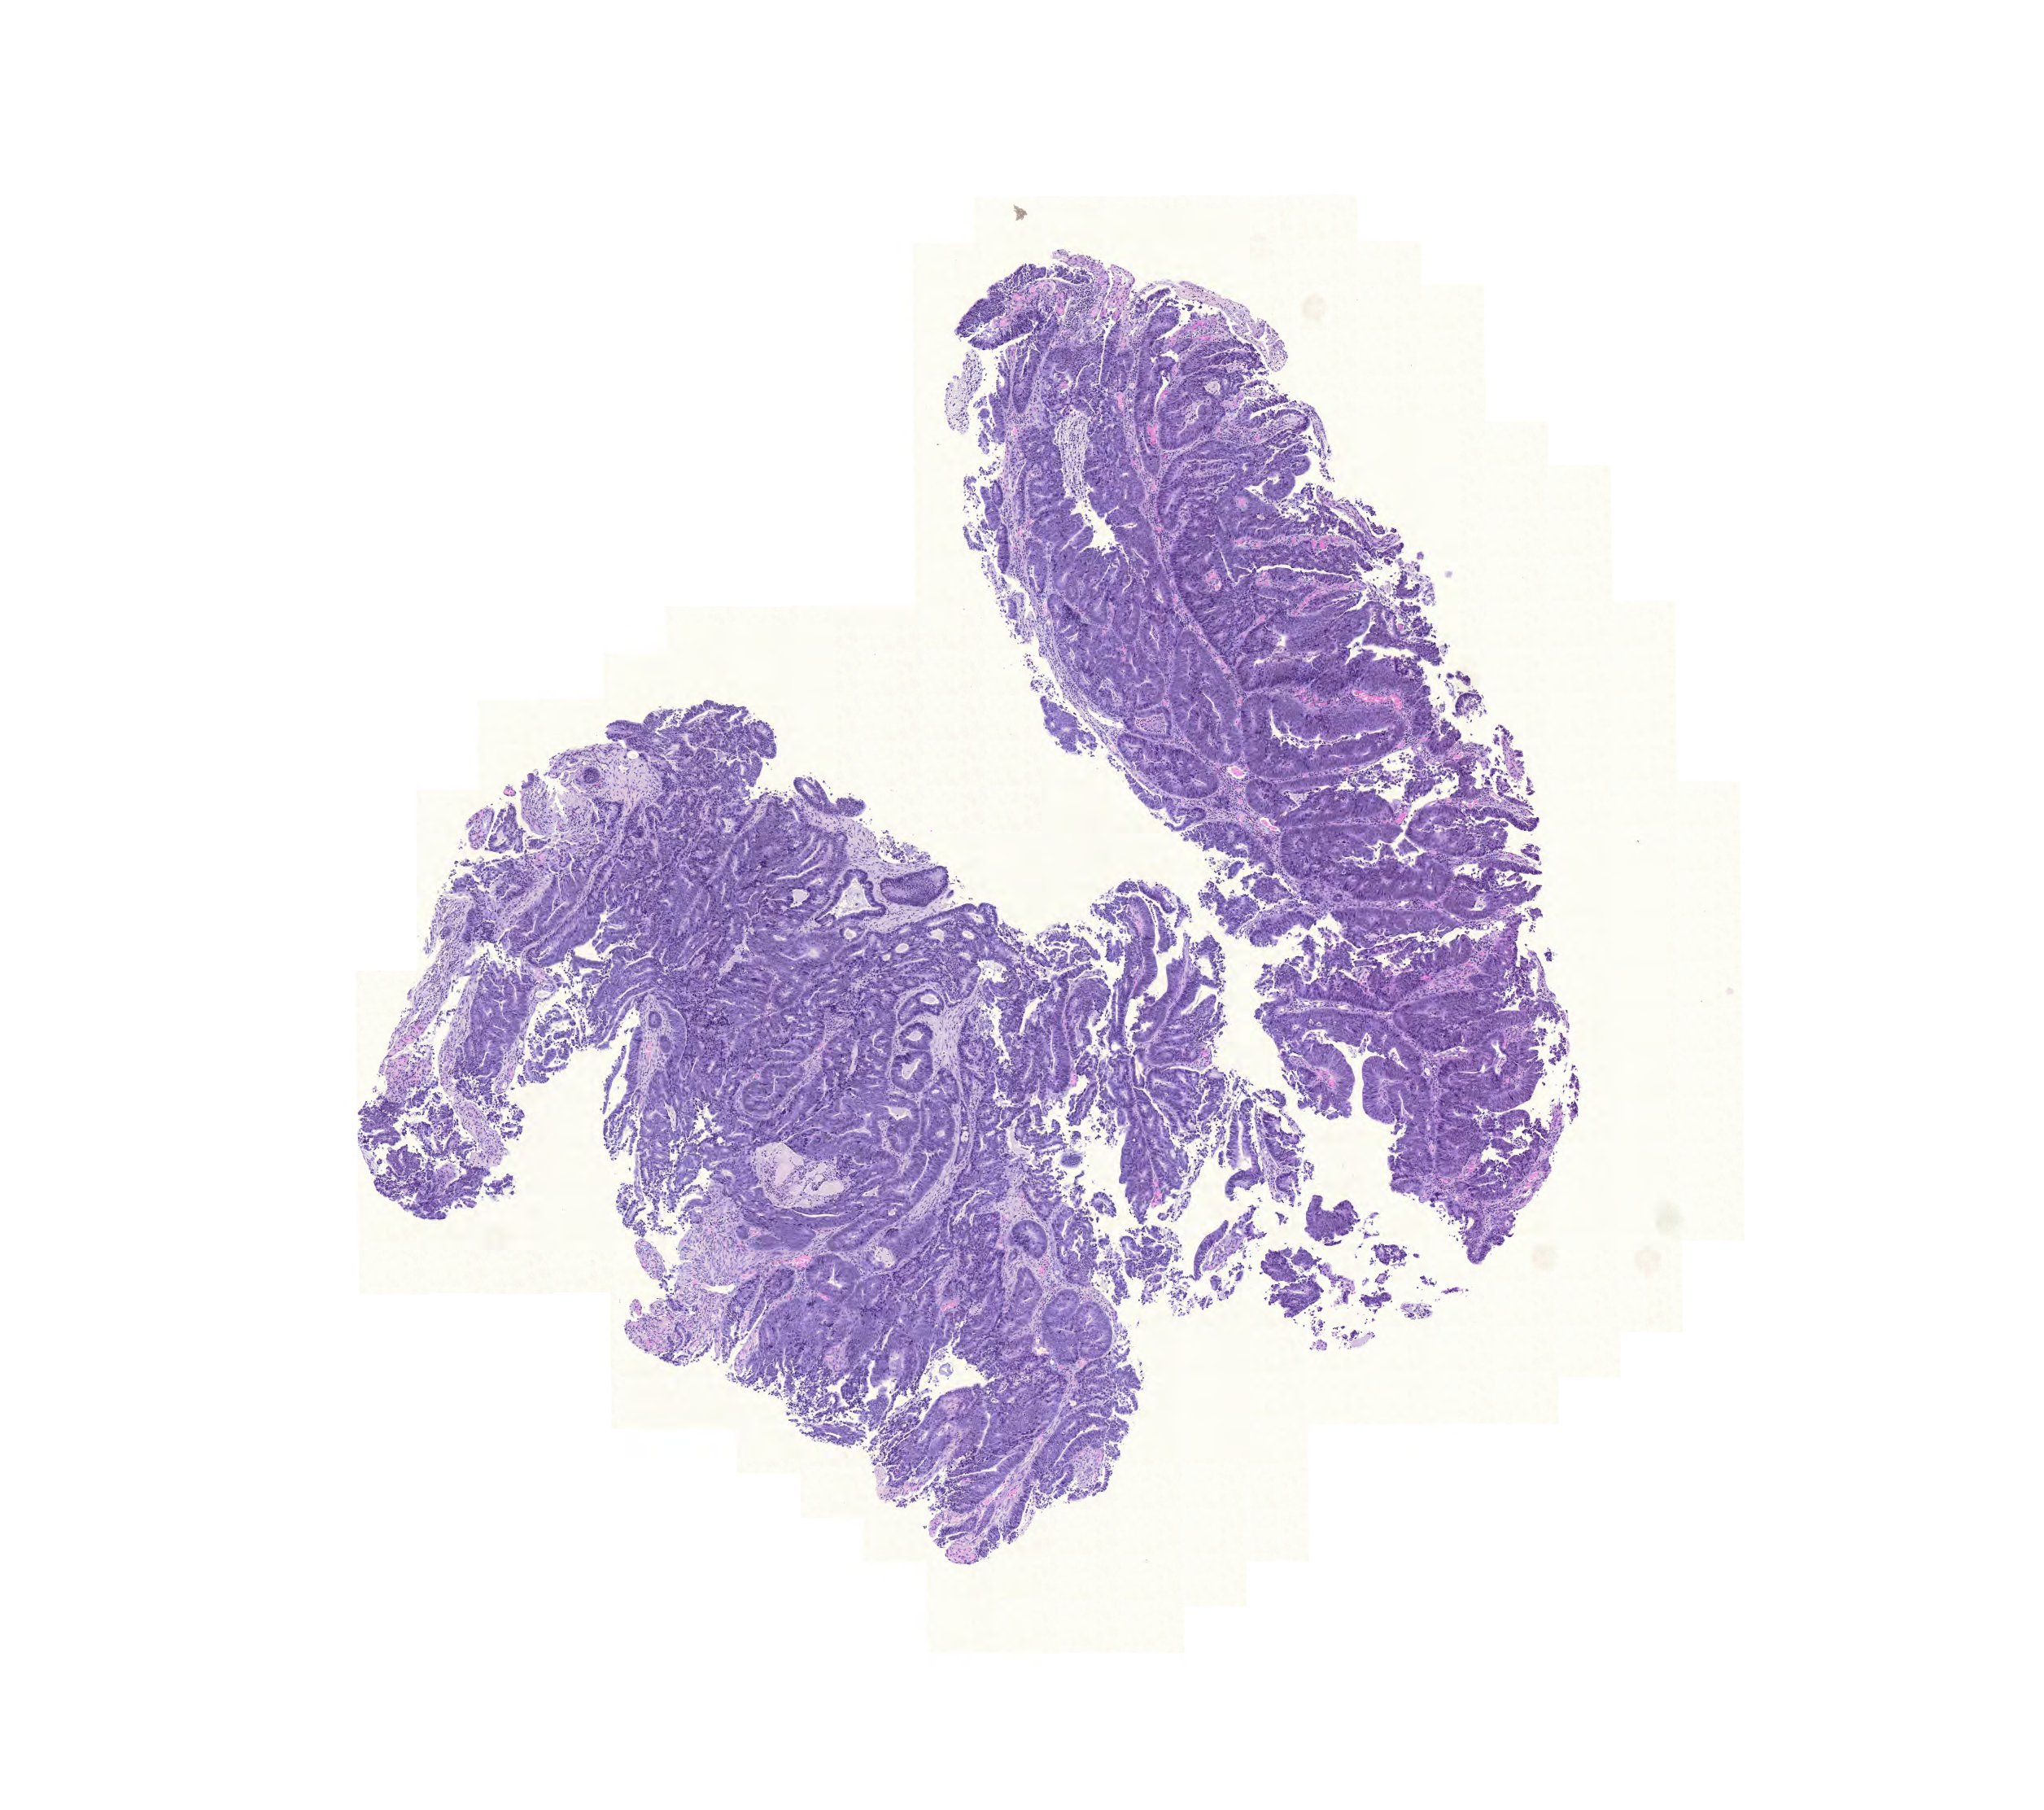
H&E whole-slide image — whole scanned area (about 9.3 x 8.3 mm, from a 20x scan) shown as a low-resolution overview. Formalin-fixed paraffin-embedded (FFPE) diagnostic section. Rectum, primary tumour sample. Male, age 68 years at initial diagnosis.
Lymph nodes positive (case pathology): 0 of 14 examined. AJCC pathologic stage: IIA (6th edition). Histologic diagnosis: Mucinous adenocarcinoma.